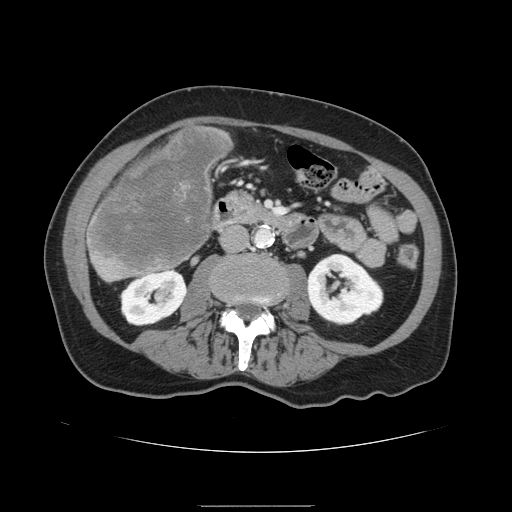
Contrast-enhanced abdominal CT, one axial slice. Position 40 of 168 along the scan axis. 120 kVp. Intravenous contrast given. Soft-tissue window (W 400 / L 40 HU). 2.5 mm slice thickness. 512 × 512 image matrix, field of view 386 × 386 mm. Male patient, age 74 years. Case-level facts recorded for this patient, not image findings: diagnosis: colorectal cancer liver metastases, imaged before liver resection; multiple liver metastases: no; largest metastasis: 14.5 cm; disease in both lobes: yes.
Structures marked on this image (expert manual segmentation):
- liver: bounding box <86,126,232,282> (left, top, right, bottom; pixels)
- liver metastasis: <91,129,229,272>